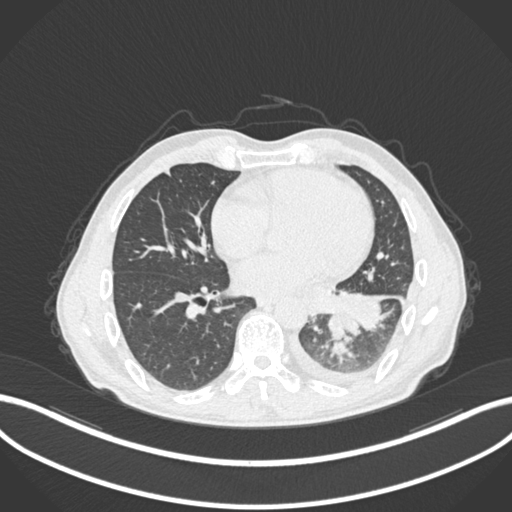
Chest CT, one axial slice; slice 99 of 222 in the series (ordered by position); reconstruction kernel B30f; lung window (W 1500 / L -600 HU); 512 × 512 image matrix, field of view 400 × 400 mm. Male patient, age 47 years. From the clinical record (not read from this slice): clinical TNM (as recorded): T3 N1 M1c.
Structures marked on this image (rectangle marked by the reading radiologist):
- lung tumour (recorded histology: small cell carcinoma): box from (x=324, y=309) to (x=359, y=343) px